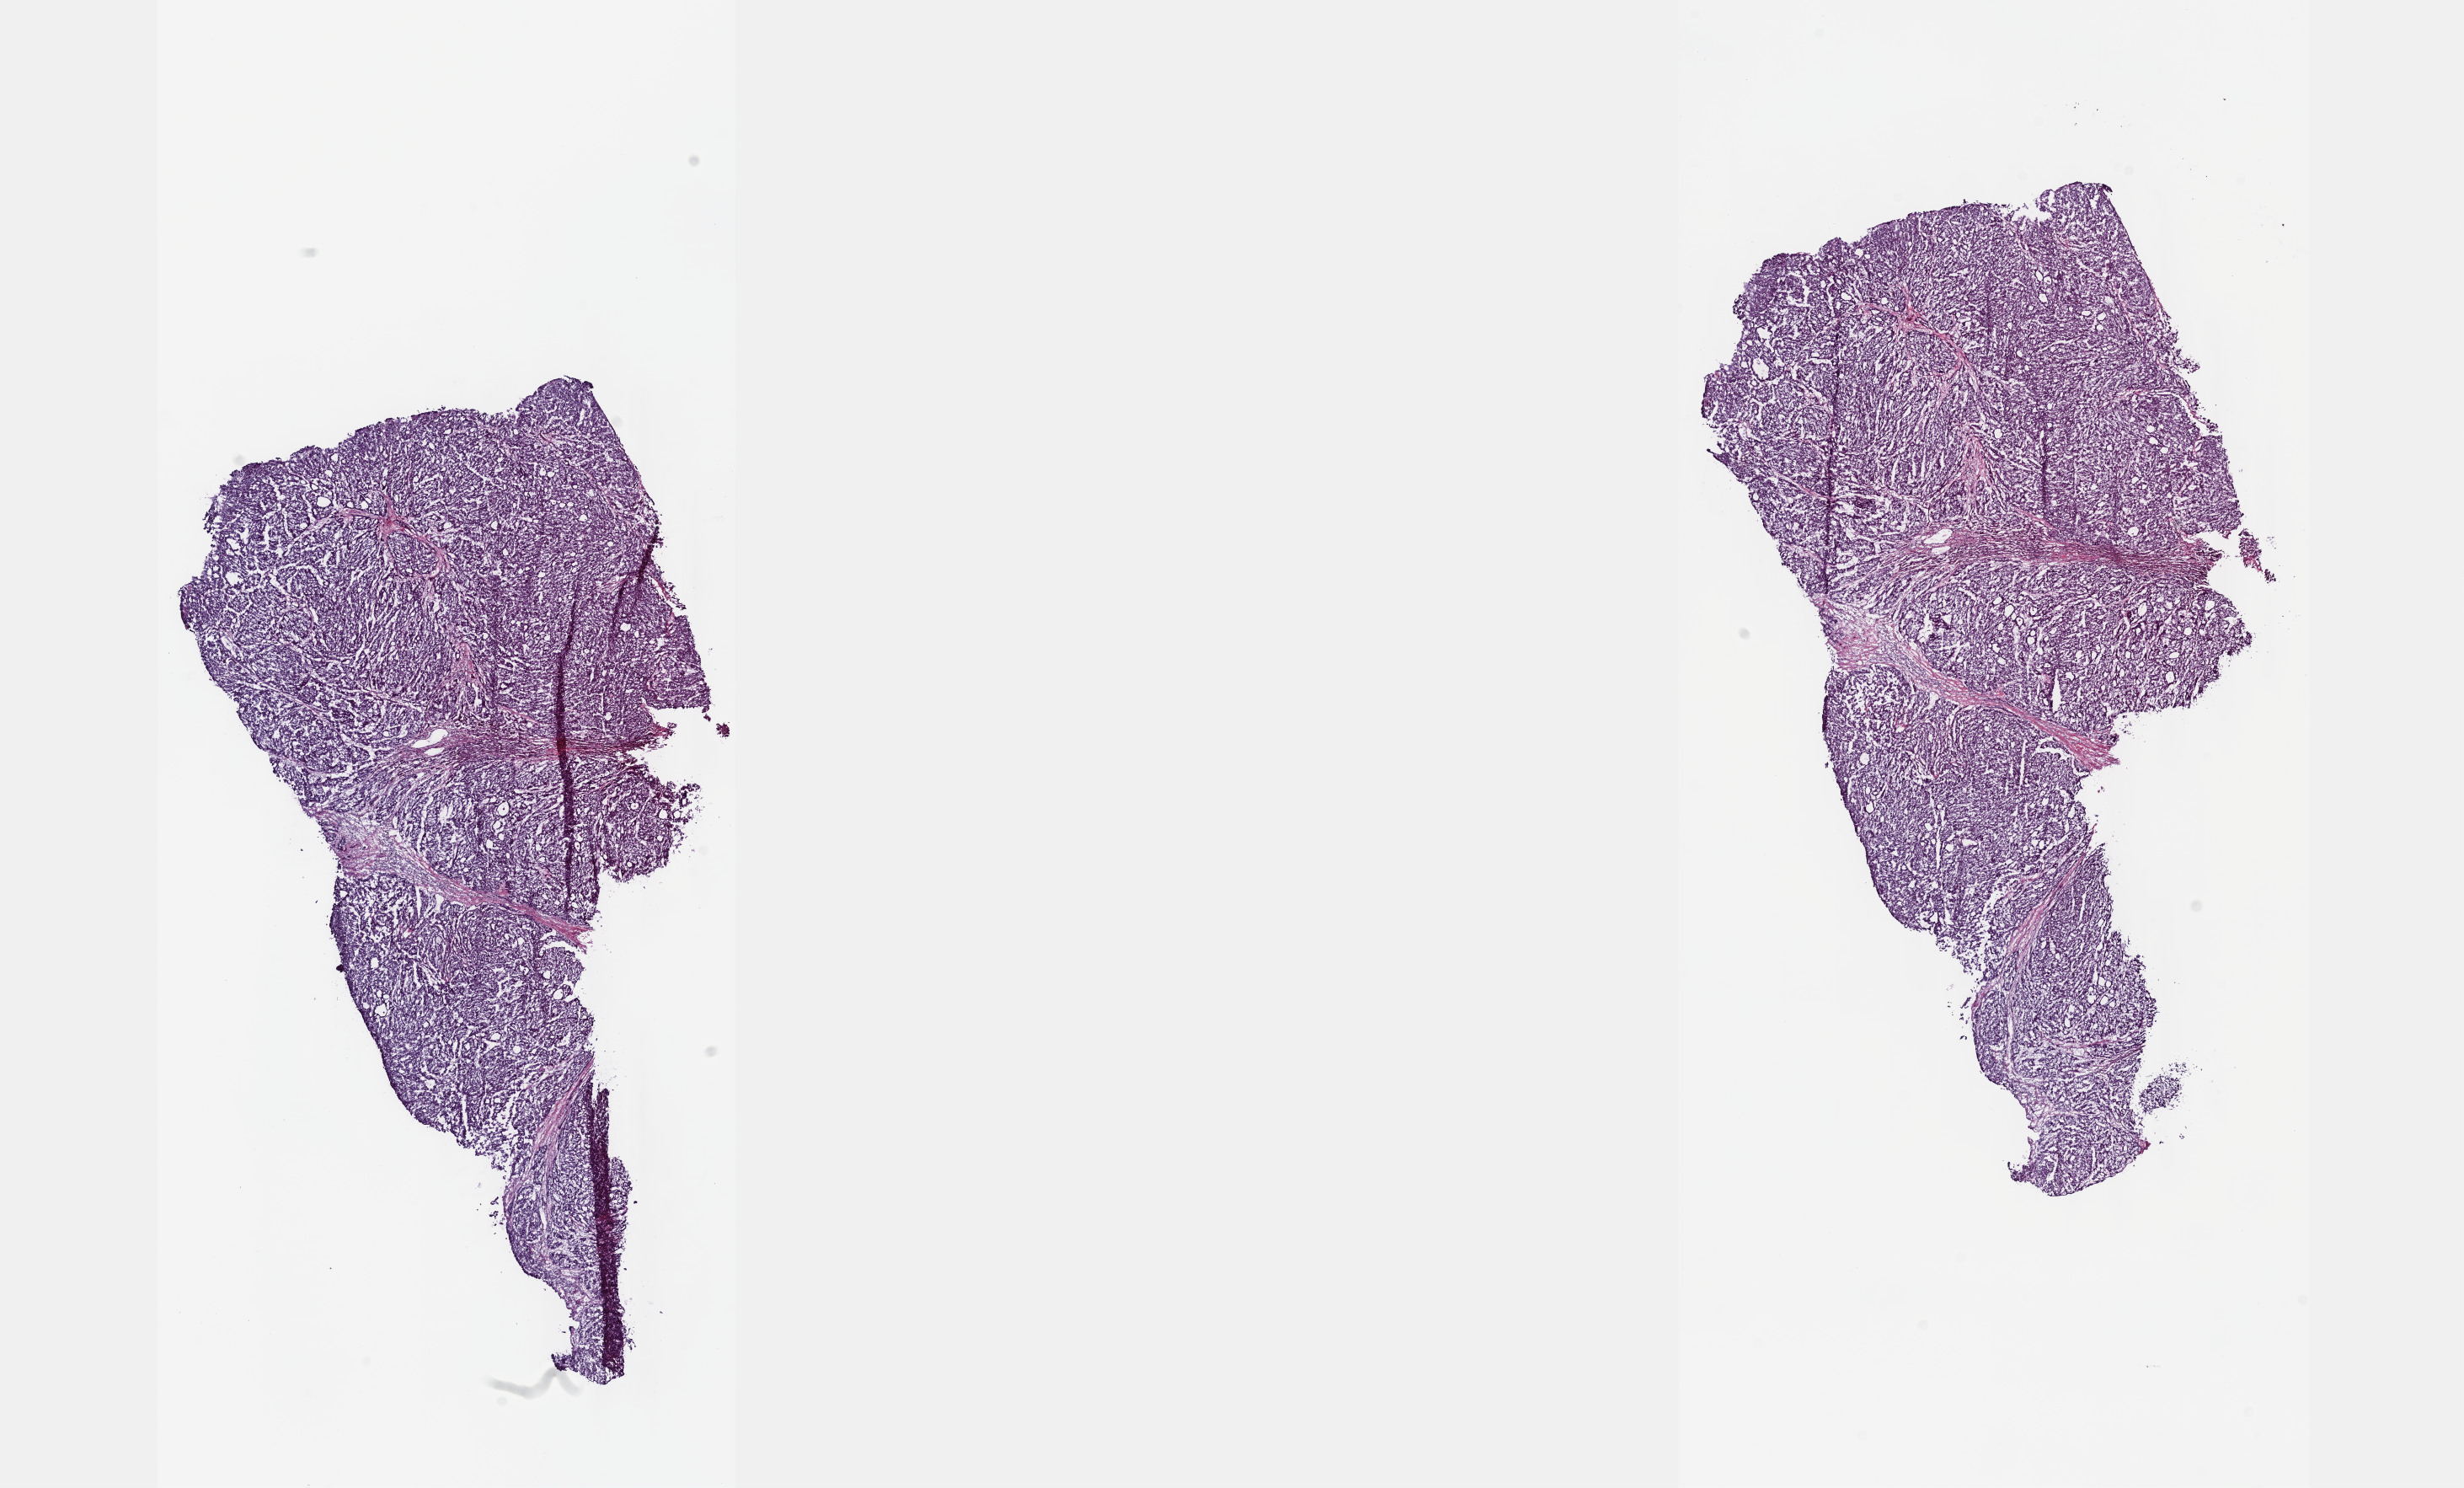
Whole-slide histology image, Hematoxylin and eosin (H&E) stained — whole scanned area (about 23.6 x 14.3 mm) shown as a low-resolution overview; frozen section from the top of the tissue portion; primary tumour sample from the bile duct. Patient: male, age at initial diagnosis 81 years. Histologic grade: G4 (undifferentiated). Composition of this section per pathologist review: tumour cells 90%, tumour nuclei 95%, normal cells 0%, stromal cells 10%, necrosis 0%. Infiltration values recorded for this section: lymphocyte infiltration 0%, monocyte infiltration 0%, neutrophil infiltration 0%.
- pathologic diagnosis: Cholangiocarcinoma (intrahepatic bile duct)
- AJCC pathologic stage: II (7th edition)